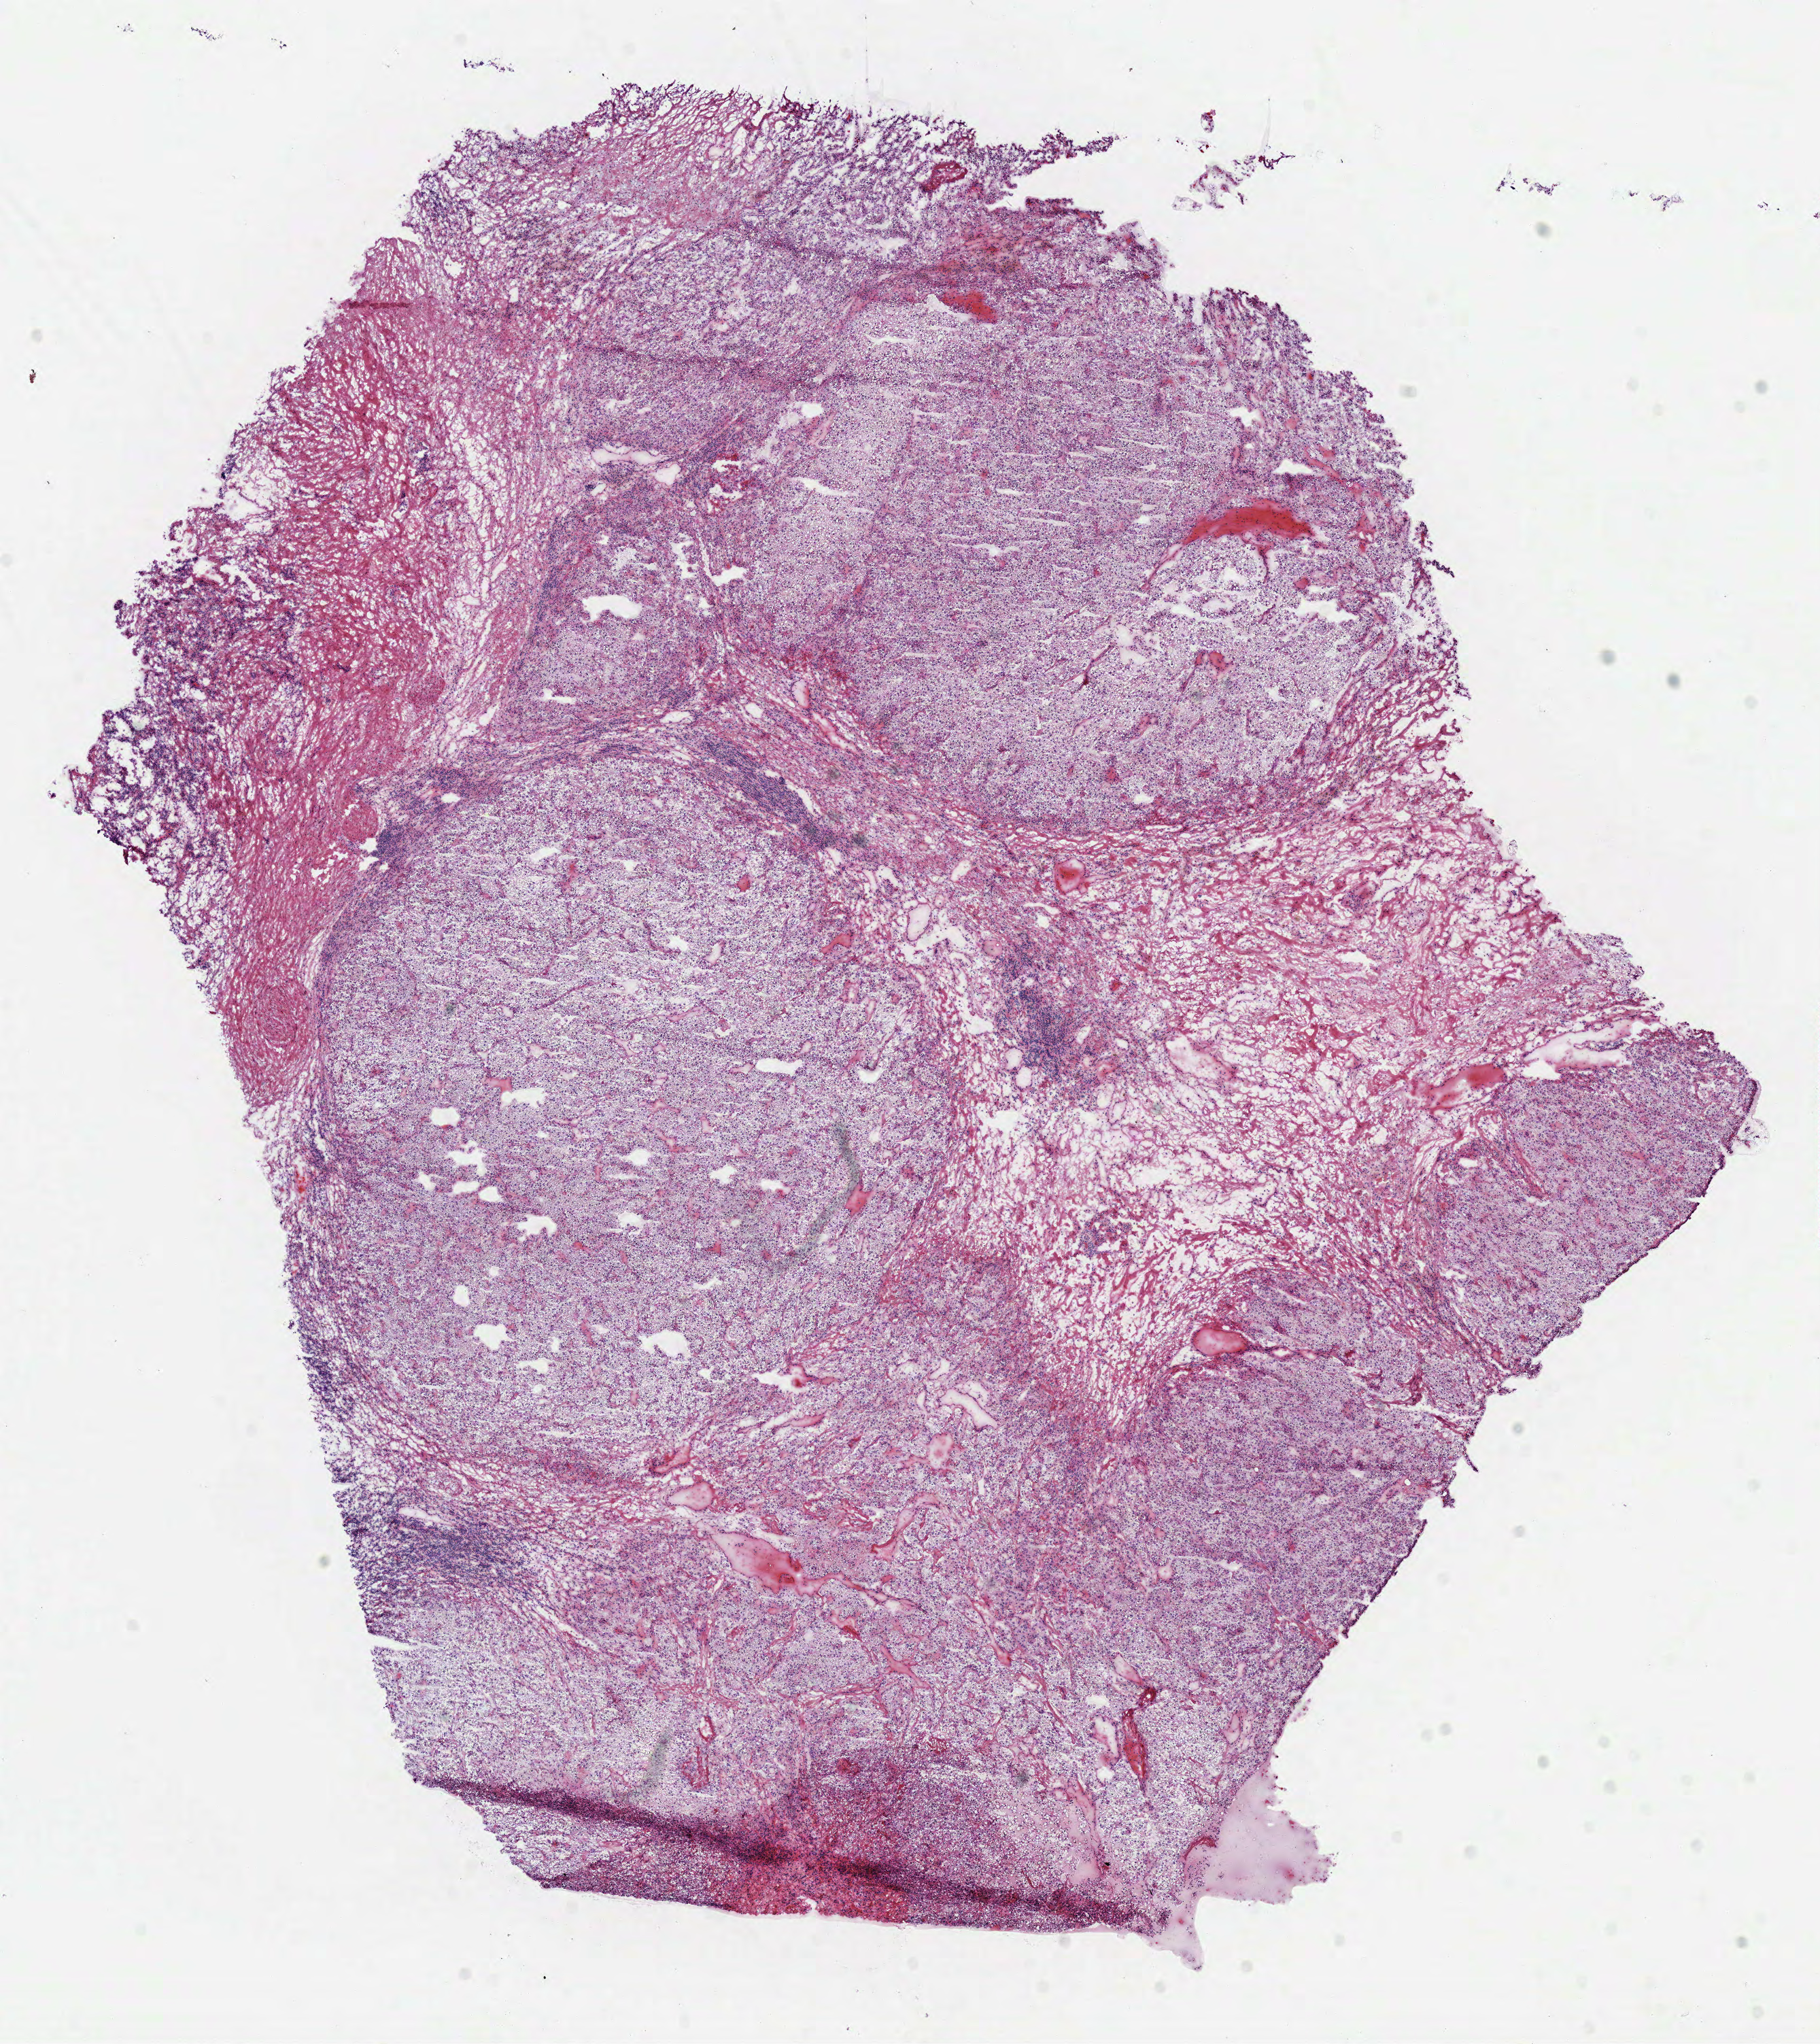
H&E-stained whole-slide image — a low-resolution overview of the entire scanned area, about 10.5 x 11.8 mm; frozen section from the top of the tissue portion; sample: primary tumour, kidney. Male, age 32 years at initial diagnosis. Composition of this section per pathologist review: tumour cells 80%, tumour nuclei 80%.
Histologic diagnosis: Clear cell adenocarcinoma, NOS.